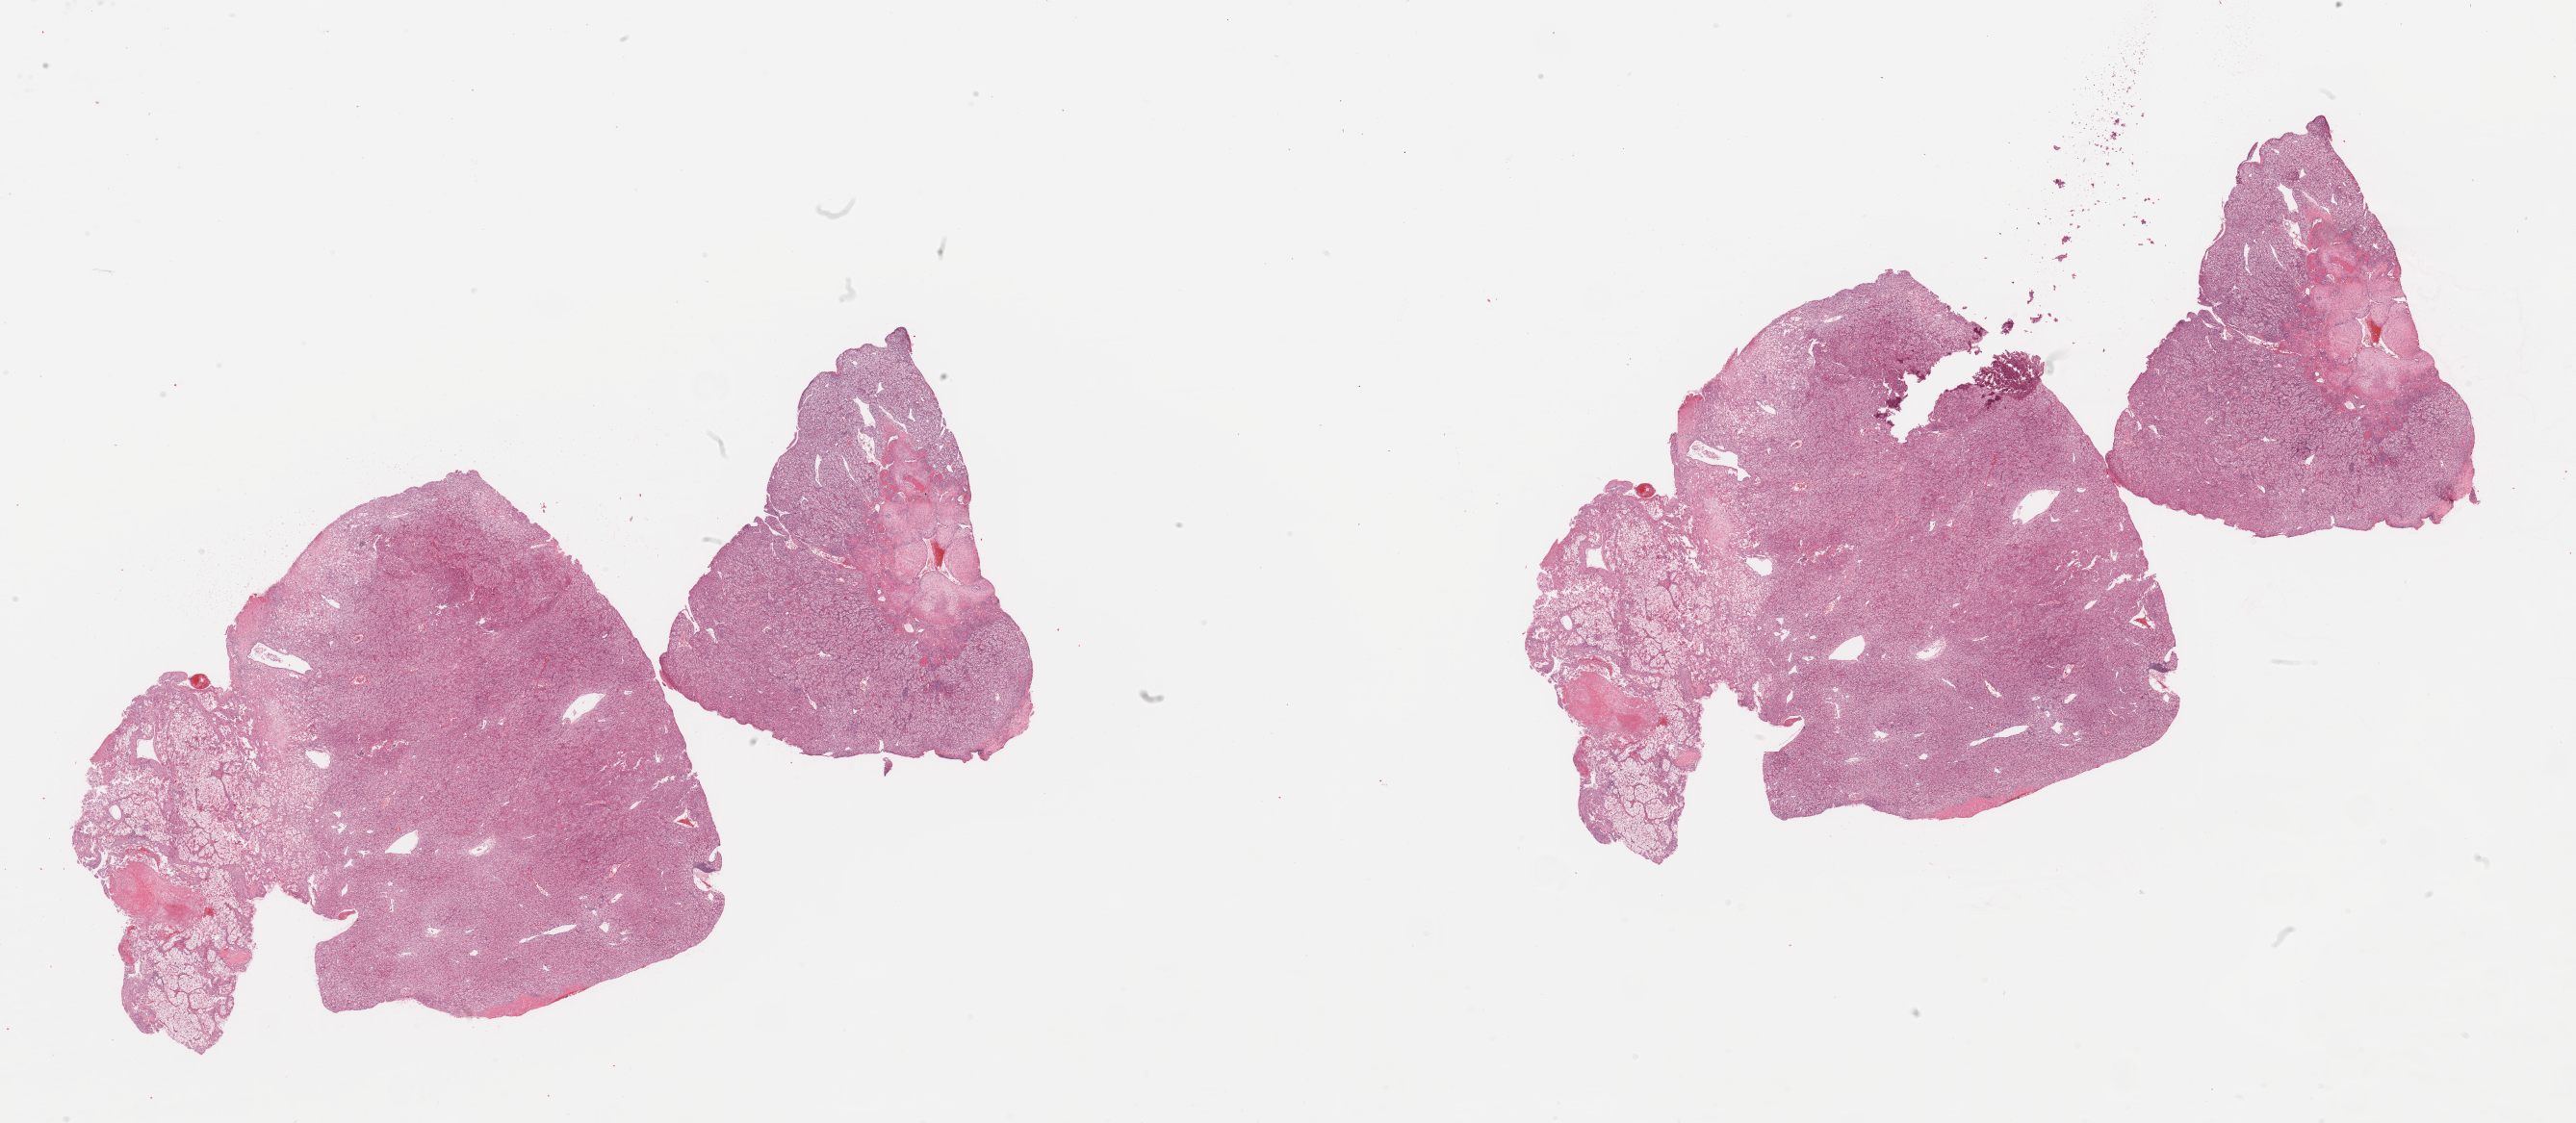
Whole-slide histology image, H&E-stained — shown as a low-resolution overview of the whole scanned area (about 42.3 x 18.5 mm); tumour tissue sample, kidney. Female, 66 y/o. Histologic grade: G4 (undifferentiated).
• AJCC pathologic stage: III
• diagnosis: Renal cell carcinoma, NOS
• primary tumour site (as recorded): lower pole